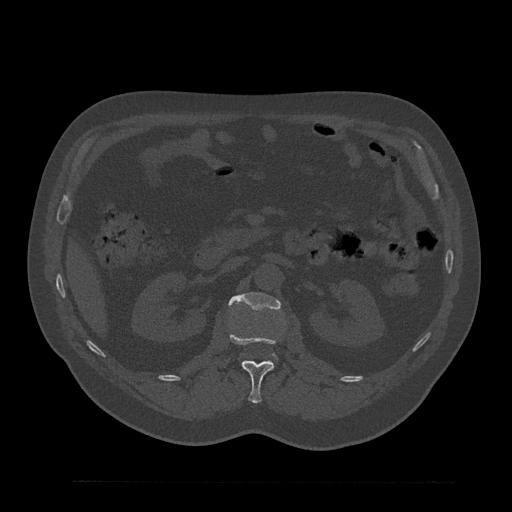
CT including the spine, one axial slice; 120 kVp; bone window (W 1800 / L 400 HU); 512 × 512 image matrix, field of view 430 × 430 mm. Male patient, age 61 years. From the clinical record (not read from this slice): primary cancer: prostate.
Structures marked on this image (semi-automatically segmented with operator editing):
- L1 vertebra: bounding box [x1, y1, x2, y2] px = [229, 333, 282, 404]
- L2 vertebra: [228, 292, 281, 310]